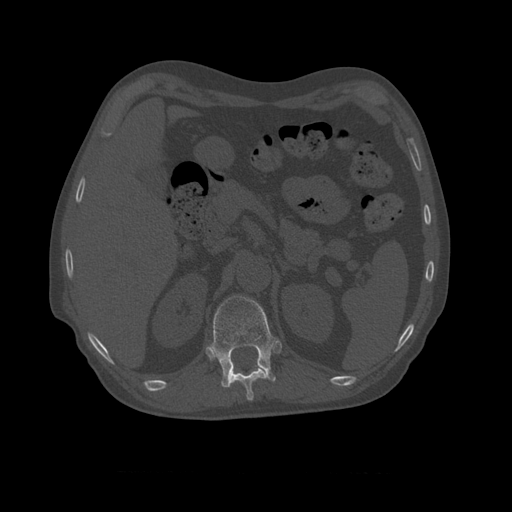
CT including the spine, one axial slice. Position 386 of 450 along the scan axis. 120 kVp. Bone window (W 1800 / L 400 HU). 1.25 mm slice thickness. 512 × 512 image matrix, field of view 405 × 405 mm. Patient age 75 years. Case-level facts recorded for this patient, not image findings: primary cancer: prostate.
Outlined on this slice (semi-automatic segmentation, software-assisted and operator-edited):
- T10 vertebra: bounding box <229,367,268,401> (left, top, right, bottom; pixels)
- T11 vertebra: <210,296,277,388>